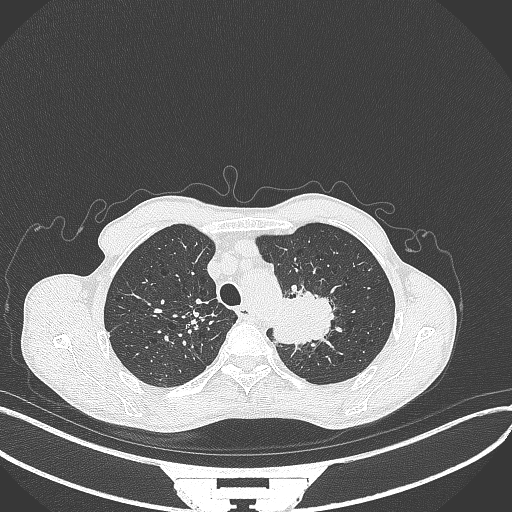
Chest CT, one axial slice. Slice 337 of 386 in the series (ordered by position). Lung window (W 1500 / L -600 HU). 512 × 512 image matrix, field of view 400 × 400 mm. Male patient, age 65 years. Case-level facts recorded for this patient, not image findings: clinical TNM (as recorded): T2b N0 M0; histopathological grade: G2.
Structures marked on this image (rectangle marked by the reading radiologist):
- lung tumour (recorded histology: adenocarcinoma): bounding box [x1, y1, x2, y2] px = [267, 285, 338, 346]